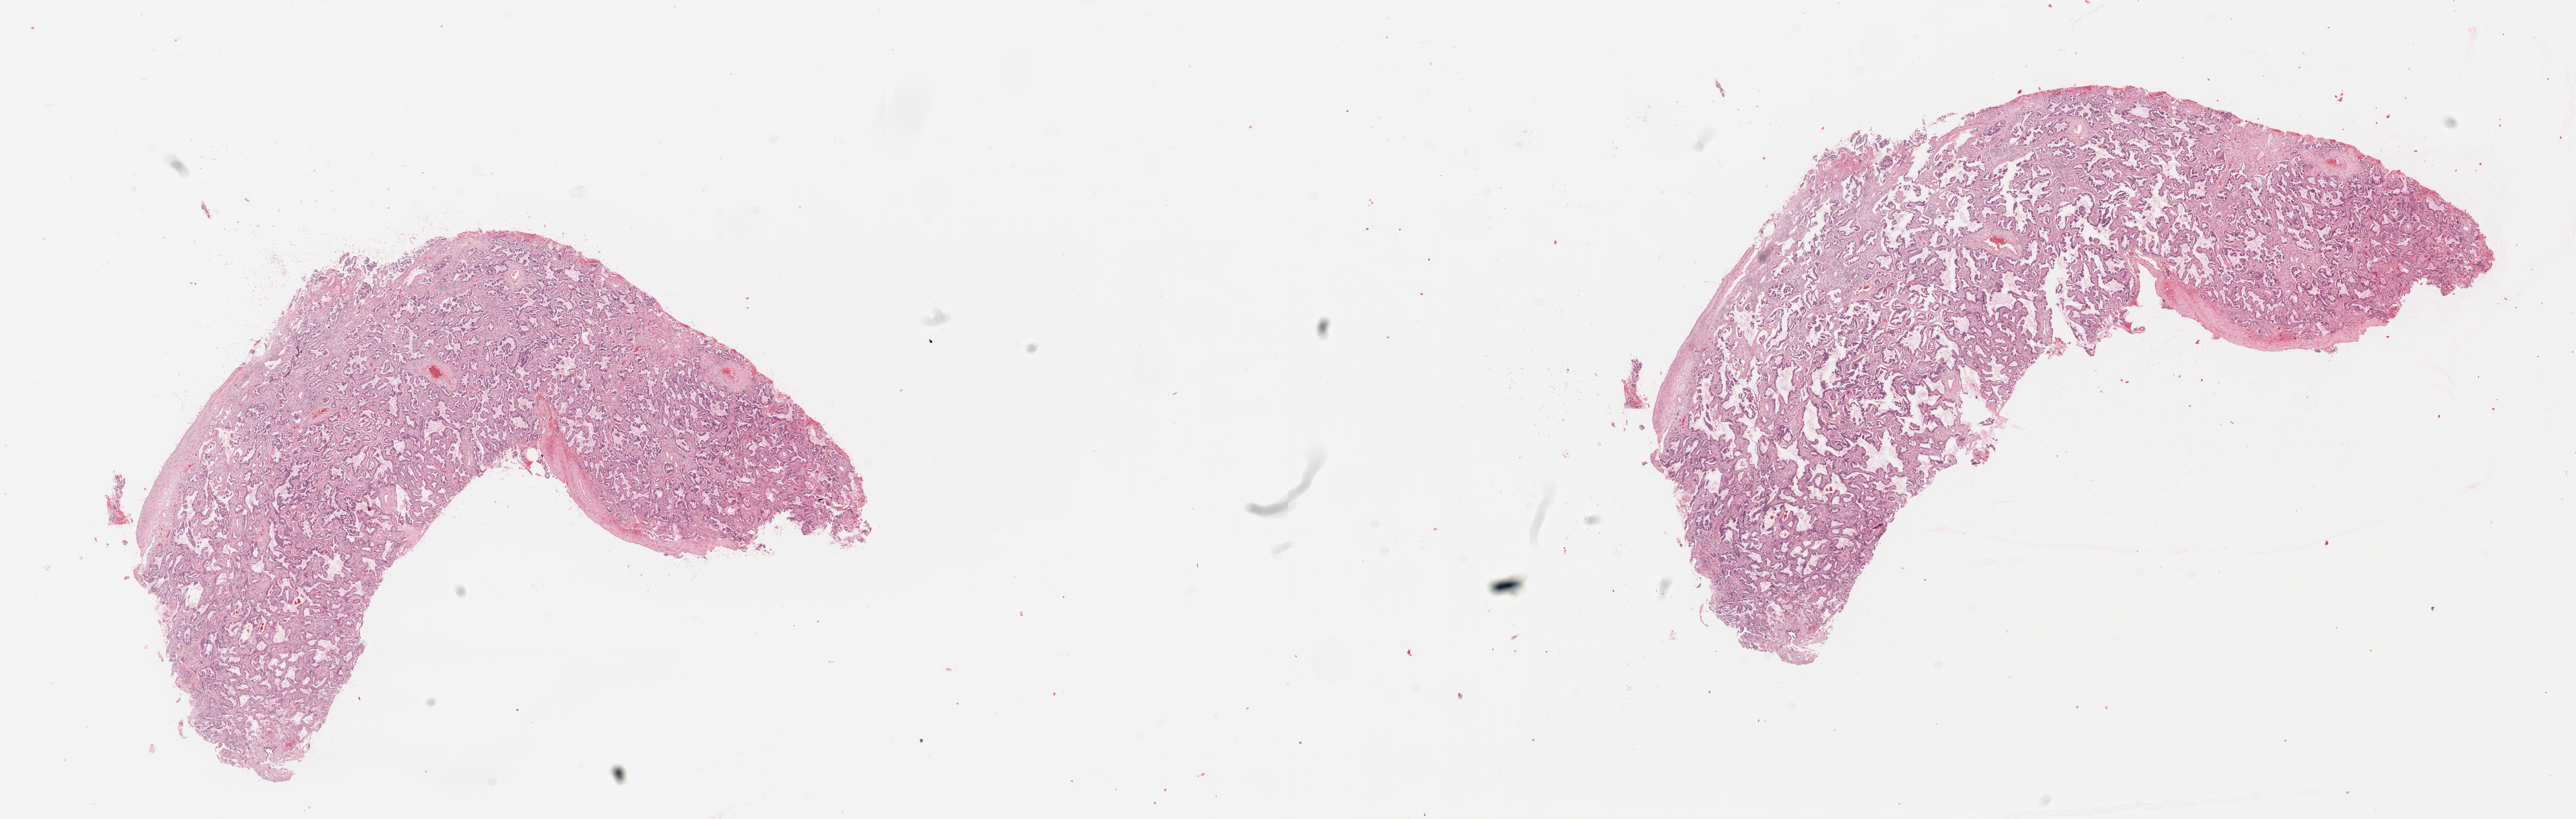
H&E whole-slide image — shown as a low-resolution overview of the whole scanned area (about 31.5 x 10.0 mm, acquisition: 20x scan), tumour tissue sample, sampled site: lung. Patient: male, age 78 years. Histologic grade: G1 (well differentiated). Pathologist review of this section (percent, as recorded): tumour nuclei 80%, necrosis 0%.
AJCC pathologic stage: IA. Histologic diagnosis: Adenocarcinoma, NOS. Primary tumour site (as recorded): right lower lobe.